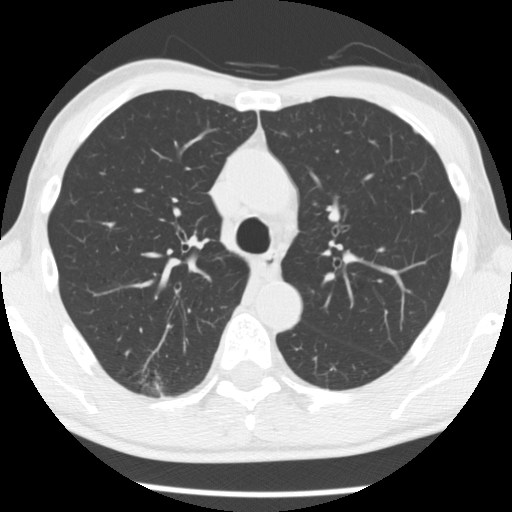
Chest CT (low-dose screening protocol), one axial image, baseline annual screen, lung window (W 1500 / L -600 HU), 2.5 mm slice thickness, standard (soft-tissue) reconstruction kernel (STANDARD), slice 90 of 277 in the series, 512 × 512 image matrix. Male participant, aged 66 years at enrolment.
Expert reader's lesion annotation, bounding box [x1, y1, x2, y2] px = [129, 356, 192, 406]. The screening reader recorded 4 non-calcified nodules or masses ≥4 mm on this exam; which of them this box marks is not recorded. Official screen result: positive, change unspecified: nodule(s) >= 4 mm or enlarging nodule(s), mass(es), or other non-specific abnormalities suspicious for lung cancer. Participant outcome: lung cancer diagnosed 503 days after this screen — adenocarcinoma, NOS, right upper lobe, undifferentiated (G4), stage IA (AJCC 6th edition), 20 mm at pathology.